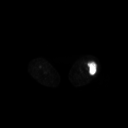
FDG PET of an extremity soft-tissue mass (from a PET/CT study), one axial slice; position 205 of 267 along the scan axis; 3.27 mm slice thickness; 128 × 128 image matrix, field of view 700 × 700 mm. Female patient, age 62 years. Case-level facts recorded for this patient, not image findings: histological type: undifferentiated – high grade; grade: high; site of the primary tumour: left thigh.
Outlined on this slice (expert contour drawn on MRI and transferred to this co-registered scan by the dataset authors):
- gross tumour volume including surrounding oedema: box from (x=84, y=60) to (x=97, y=75) px
- gross tumour volume (mass): (x=88, y=61)–(x=97, y=75)